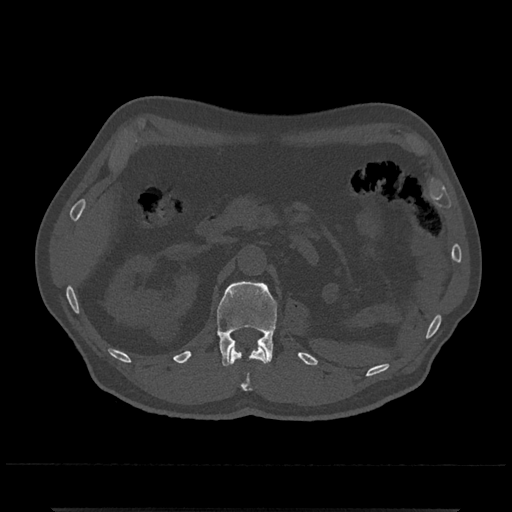
CT including the spine, one axial slice. Position 382 of 797 along the scan axis. Reconstruction kernel Br40s/3. 120 kVp. Bone window (W 1800 / L 400 HU). 512 × 512 image matrix. Male patient, age 67 years. Case-level facts recorded for this patient, not image findings: primary cancer: prostate.
Structures marked on this image (semi-automatic segmentation, software-assisted and operator-edited):
- L1 vertebra: bounding box <217,281,277,367> (left, top, right, bottom; pixels)
- T12 vertebra: <229,346,266,390>